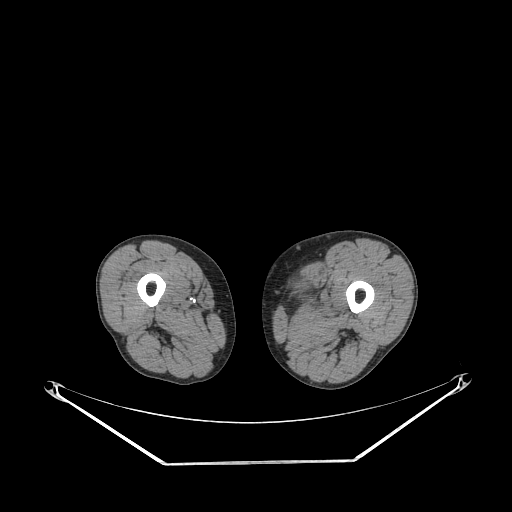
CT of an extremity soft-tissue mass (from a PET/CT study), one axial slice; position 224 of 267 along the scan axis; reconstruction kernel STANDARD; soft-tissue window (W 400 / L 40 HU); 3.75 mm slice thickness; 512 × 512 image matrix. Male patient. Case-level facts recorded for this patient, not image findings: histological type: pleiomorphic liposarcoma; grade: high; site of the primary tumour: left thigh.
Annotated regions visible in this slice (expert contour drawn on MRI and transferred to this co-registered scan by the dataset authors):
- gross tumour volume including surrounding oedema: bounding box [x1, y1, x2, y2] px = [304, 283, 337, 316]